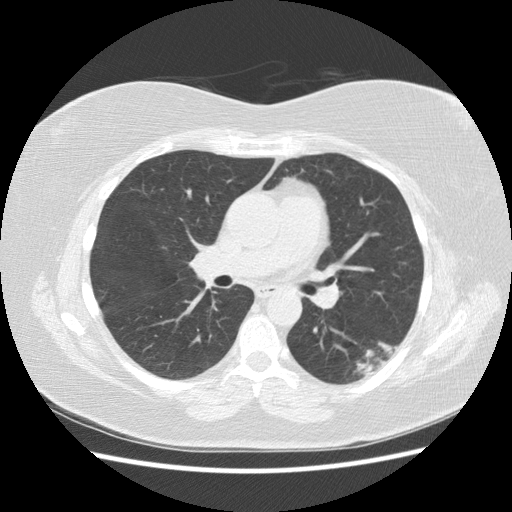
Axial slice from a low-dose chest CT screening exam. Third annual screen. Lung window (W 1500 / L -600 HU). Female participant, aged 57 years at enrolment. Current smoker at enrolment.
Expert-annotated lung lesion, bounding box [x1, y1, x2, y2] px = [330, 326, 412, 387]. The exam's reader record, not a measurement of the box and not confirmed to be the same lesion: non-calcified nodule or mass ≥4 mm, left lower lobe, 40 × 20 mm, poorly defined margins, mixed attenuation, pre-existing on the prior screen: yes; interval growth: yes. Later outcome: lung cancer diagnosed 55 days after this screen — squamous cell carcinoma, NOS, left lower lobe, poorly differentiated (G3), stage IB (AJCC 6th edition), 40 mm at pathology.